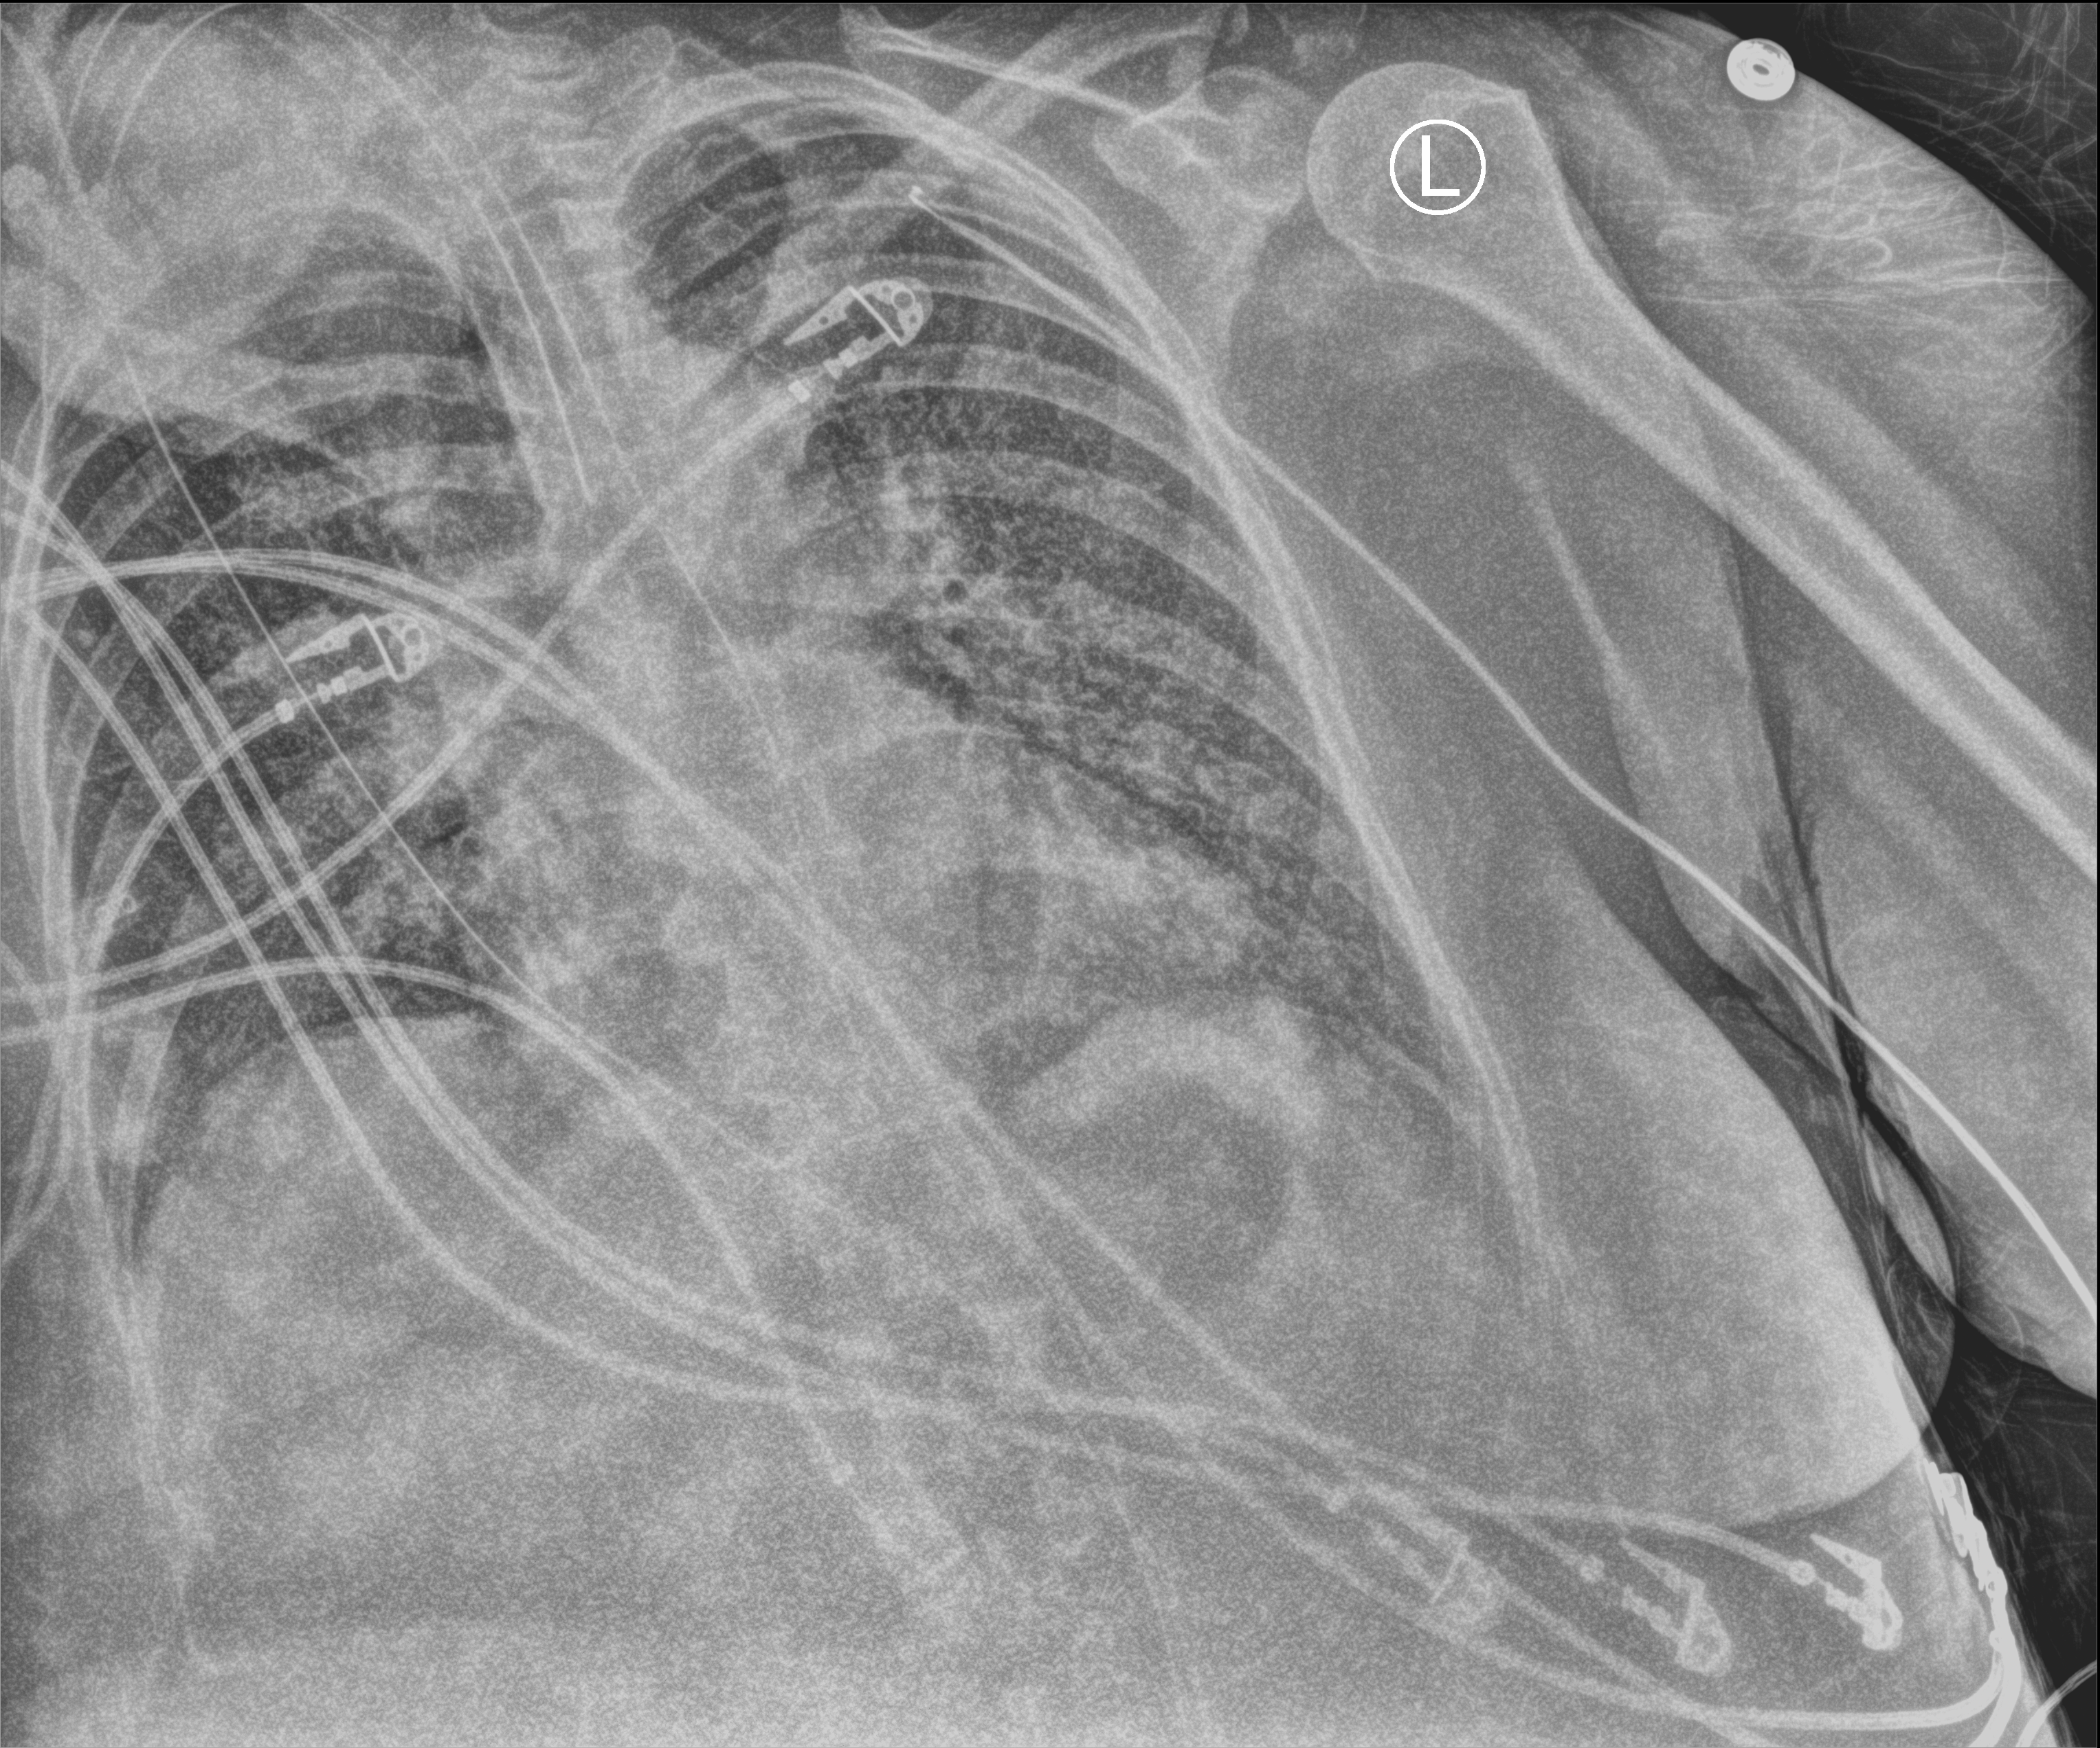
Portable chest radiograph. Patient hospitalised with COVID-19; female, aged 60–74 years.
From the hospital-stay record, not from the radiograph (when in the stay this image was taken is not recorded): other chronic lung disease (admission record): no.